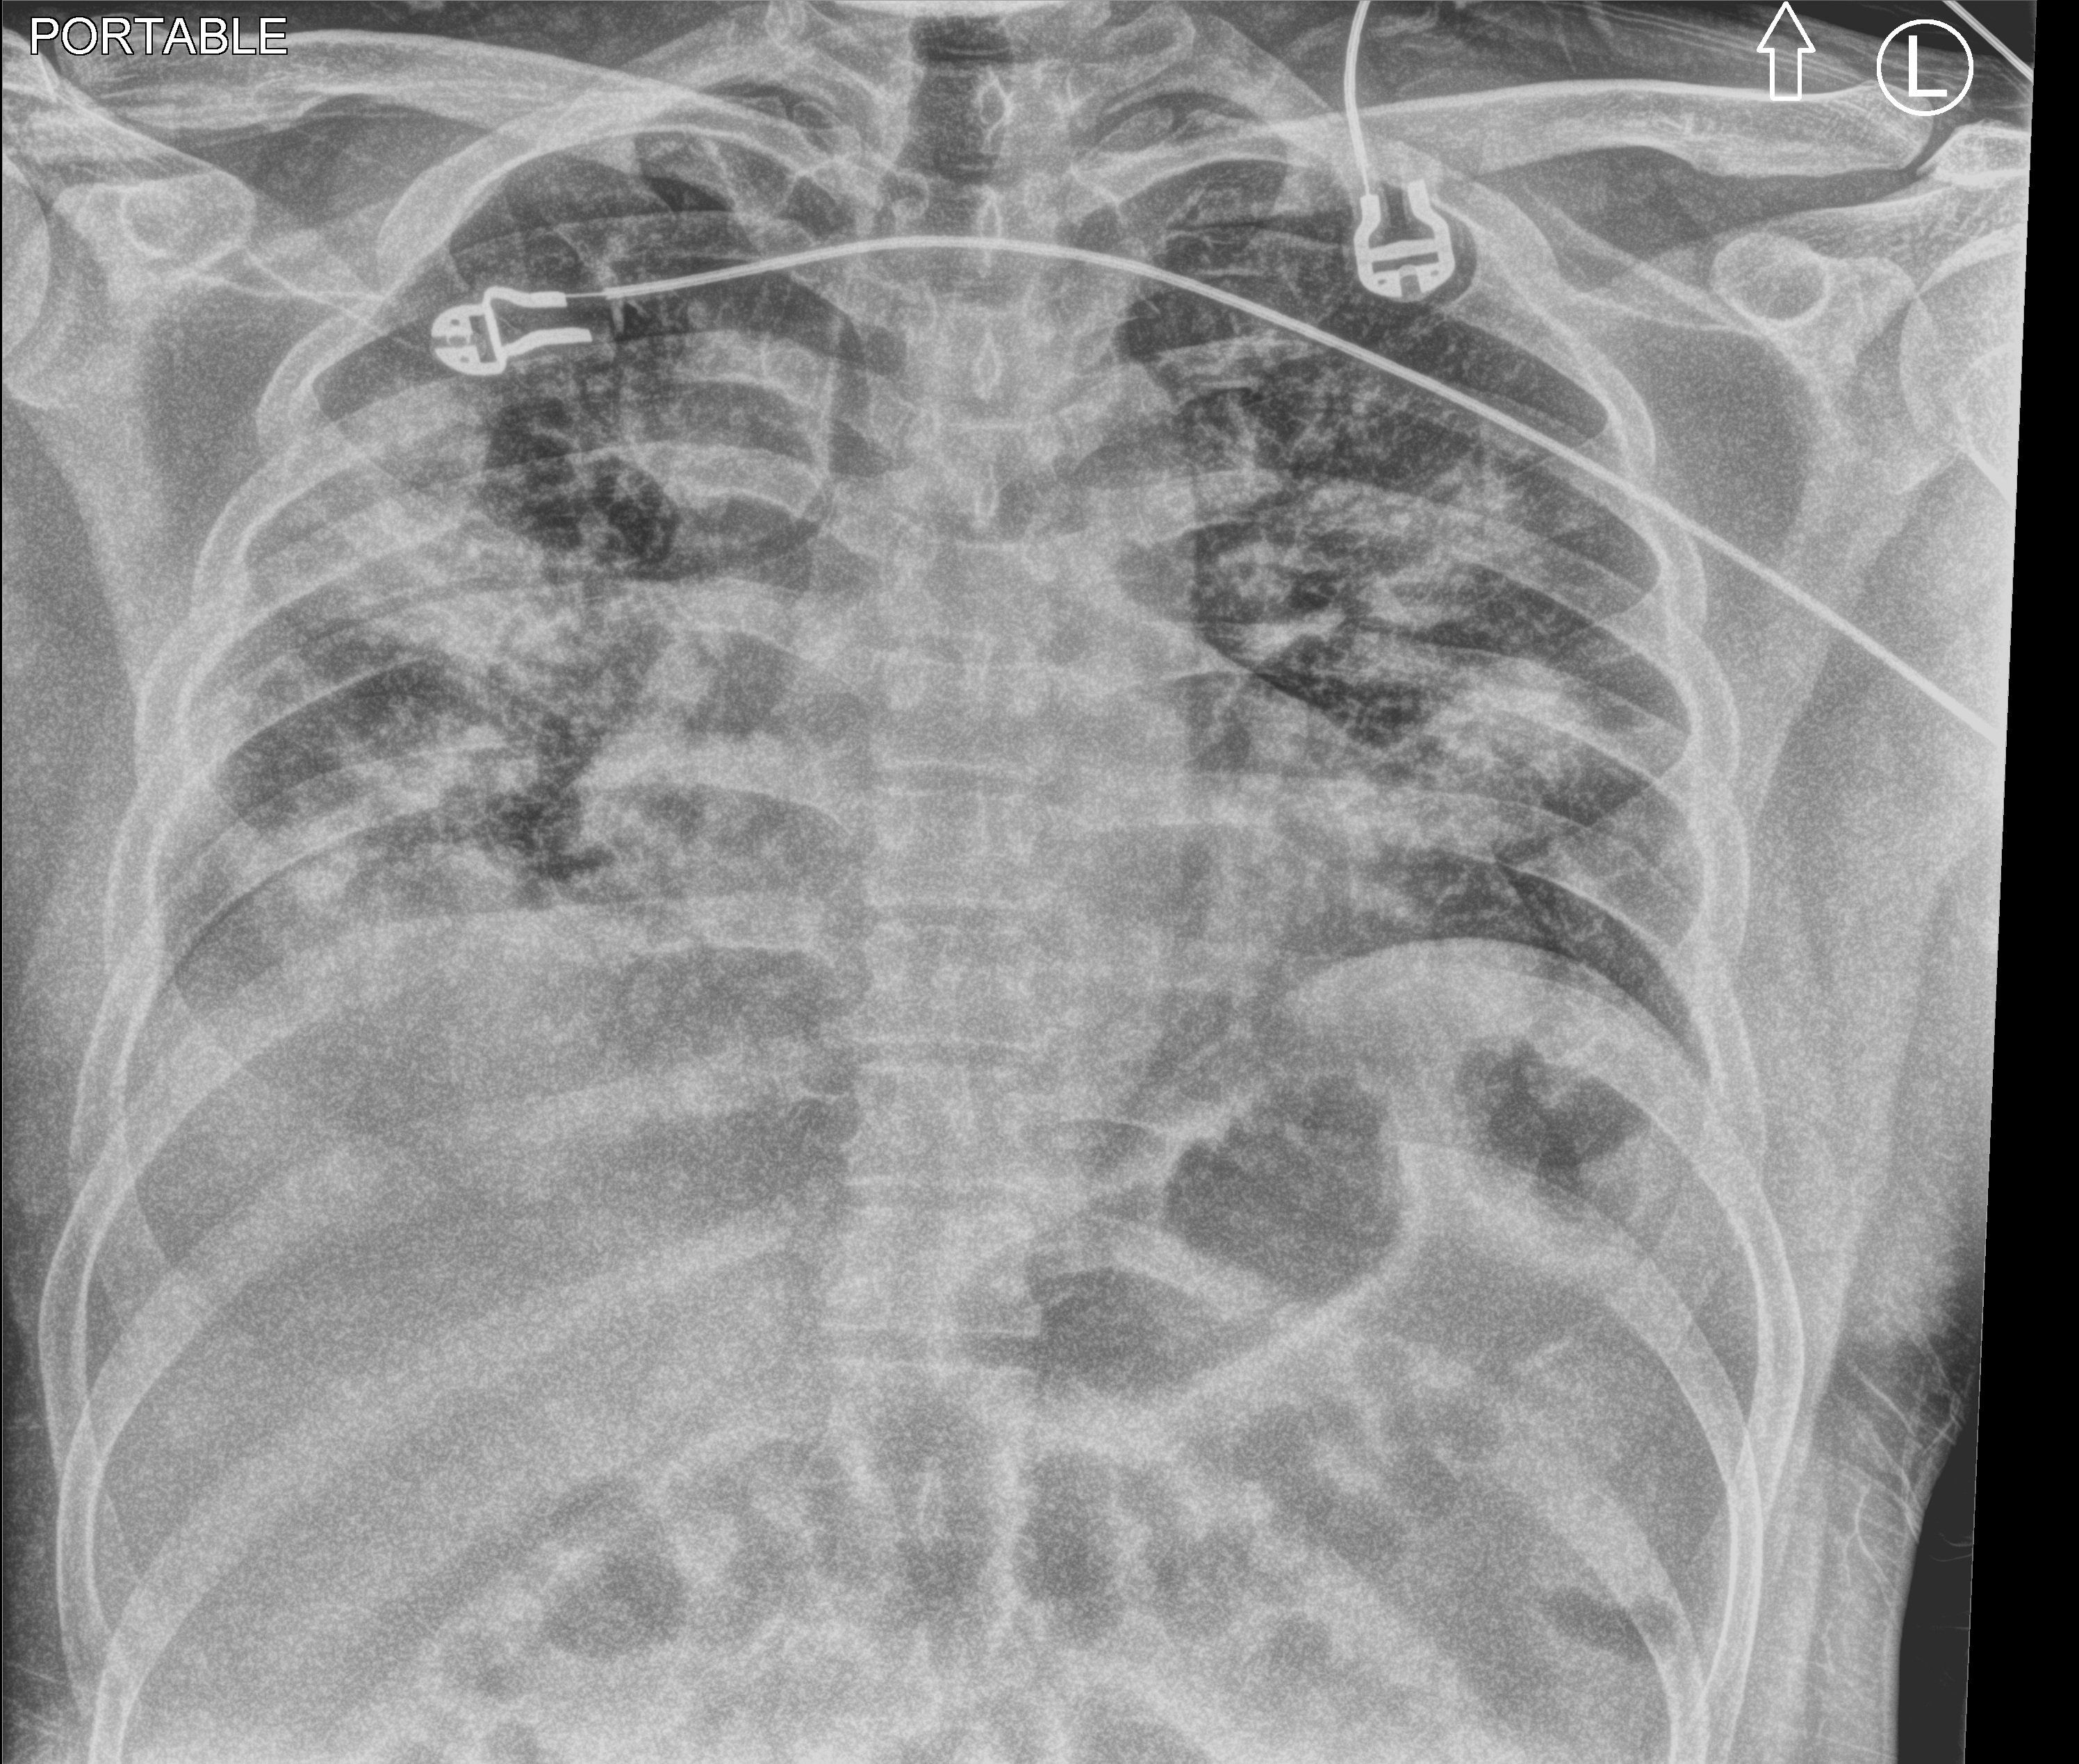
Portable chest radiograph, anteroposterior (AP) projection. Male patient hospitalised with COVID-19, age 18–59 years.
Hospital-stay facts (about this admission, not read from this image; timing relative to this image not recorded): mechanically ventilated during this hospital stay: no.